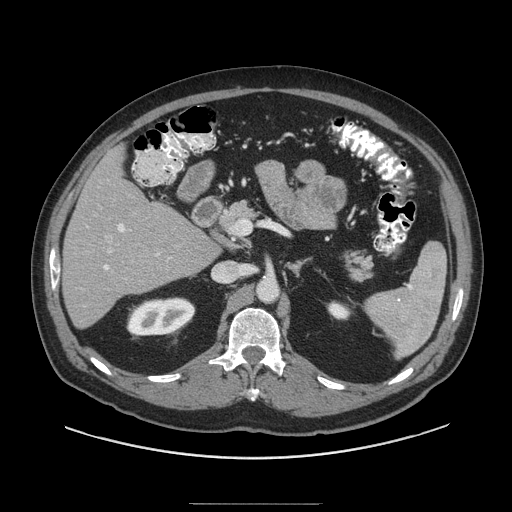
Contrast-enhanced abdominal CT (liver protocol), one axial slice. Slice 49 of 91 in the series (ordered by position). Reconstruction kernel STANDARD. 140 kVp. Soft-tissue window (W 400 / L 40 HU). 2.5 mm slice thickness. 512 × 512 image matrix, field of view 440 × 440 mm. Case-level facts recorded for this patient, not image findings: diagnosis: hepatocellular carcinoma (patient treated with transarterial chemoembolisation; whether this scan precedes or follows treatment is not stated here); TNM stage (as recorded): Stage-I.
Annotated regions visible in this slice (semi-automatically segmented with operator editing):
- liver parenchyma outside the tumour (the mass and vessels are separate outlines, so this box may not span the whole liver): box from (x=62, y=146) to (x=218, y=328) px
- liver vessels: (x=104, y=223)–(x=159, y=270)